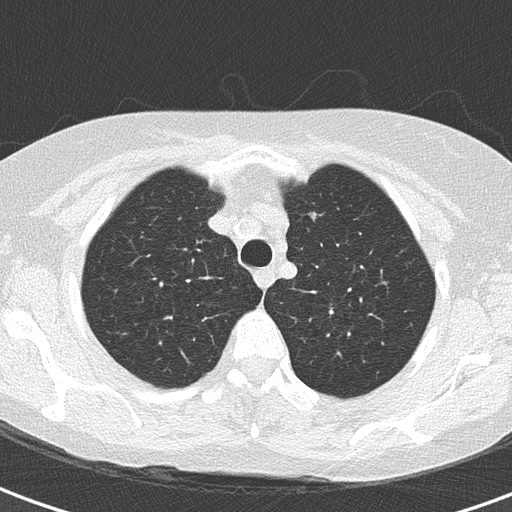
Axial slice from a low-dose chest CT screening exam. Baseline annual screen. Lung window (W 1500 / L -600 HU). Lung (sharp) reconstruction kernel (B50f). Slice 36 of 172 in the series. Female participant, aged 64 years at enrolment.
Expert-annotated lung lesion, box from (x=291, y=200) to (x=335, y=235) px. Screening reader's record for this exam: no non-calcified nodule ≥4 mm recorded. Later outcome: lung cancer diagnosed 508 days after this screen (after the second annual screen) — adenocarcinoma, NOS, left upper lobe, moderately differentiated (G2), stage IA (AJCC 6th edition), 7 mm at pathology.